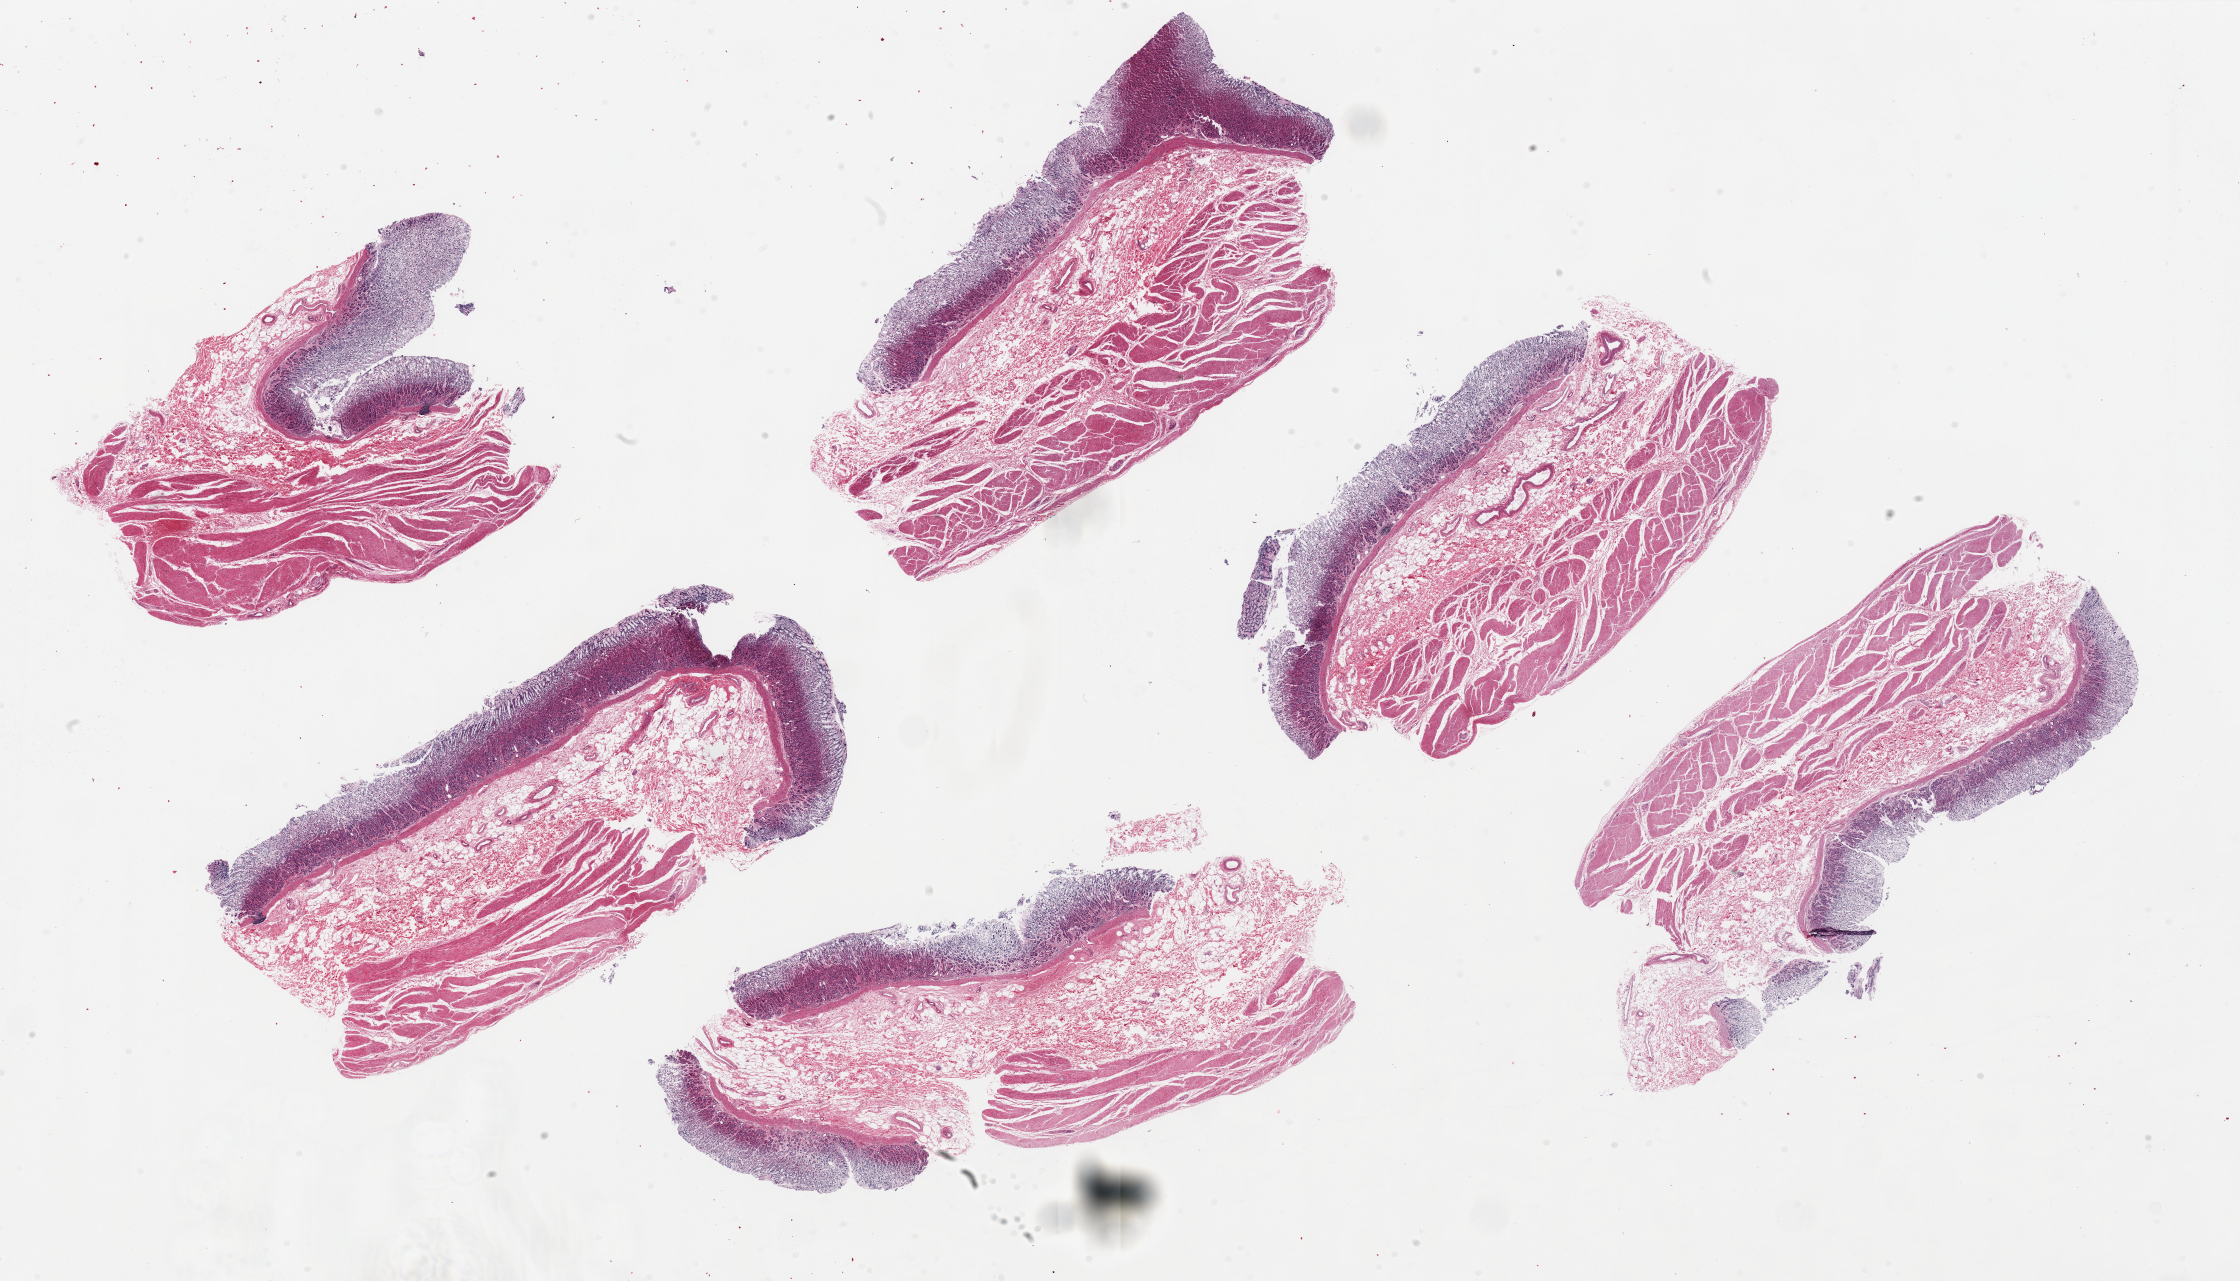
Digitized H&E-stained section, brightfield, whole scanned area (about 35.4 x 20.3 mm) shown as a low-resolution overview, PAXgene-fixed paraffin-embedded (PFPE) section, section of stomach (target tissue), donor tissue sample.
Reviewer comment on this tissue sample: 6 ~10x4mm pieces; mucosa is ~25% specimen thickness but with partial-total autolysis.